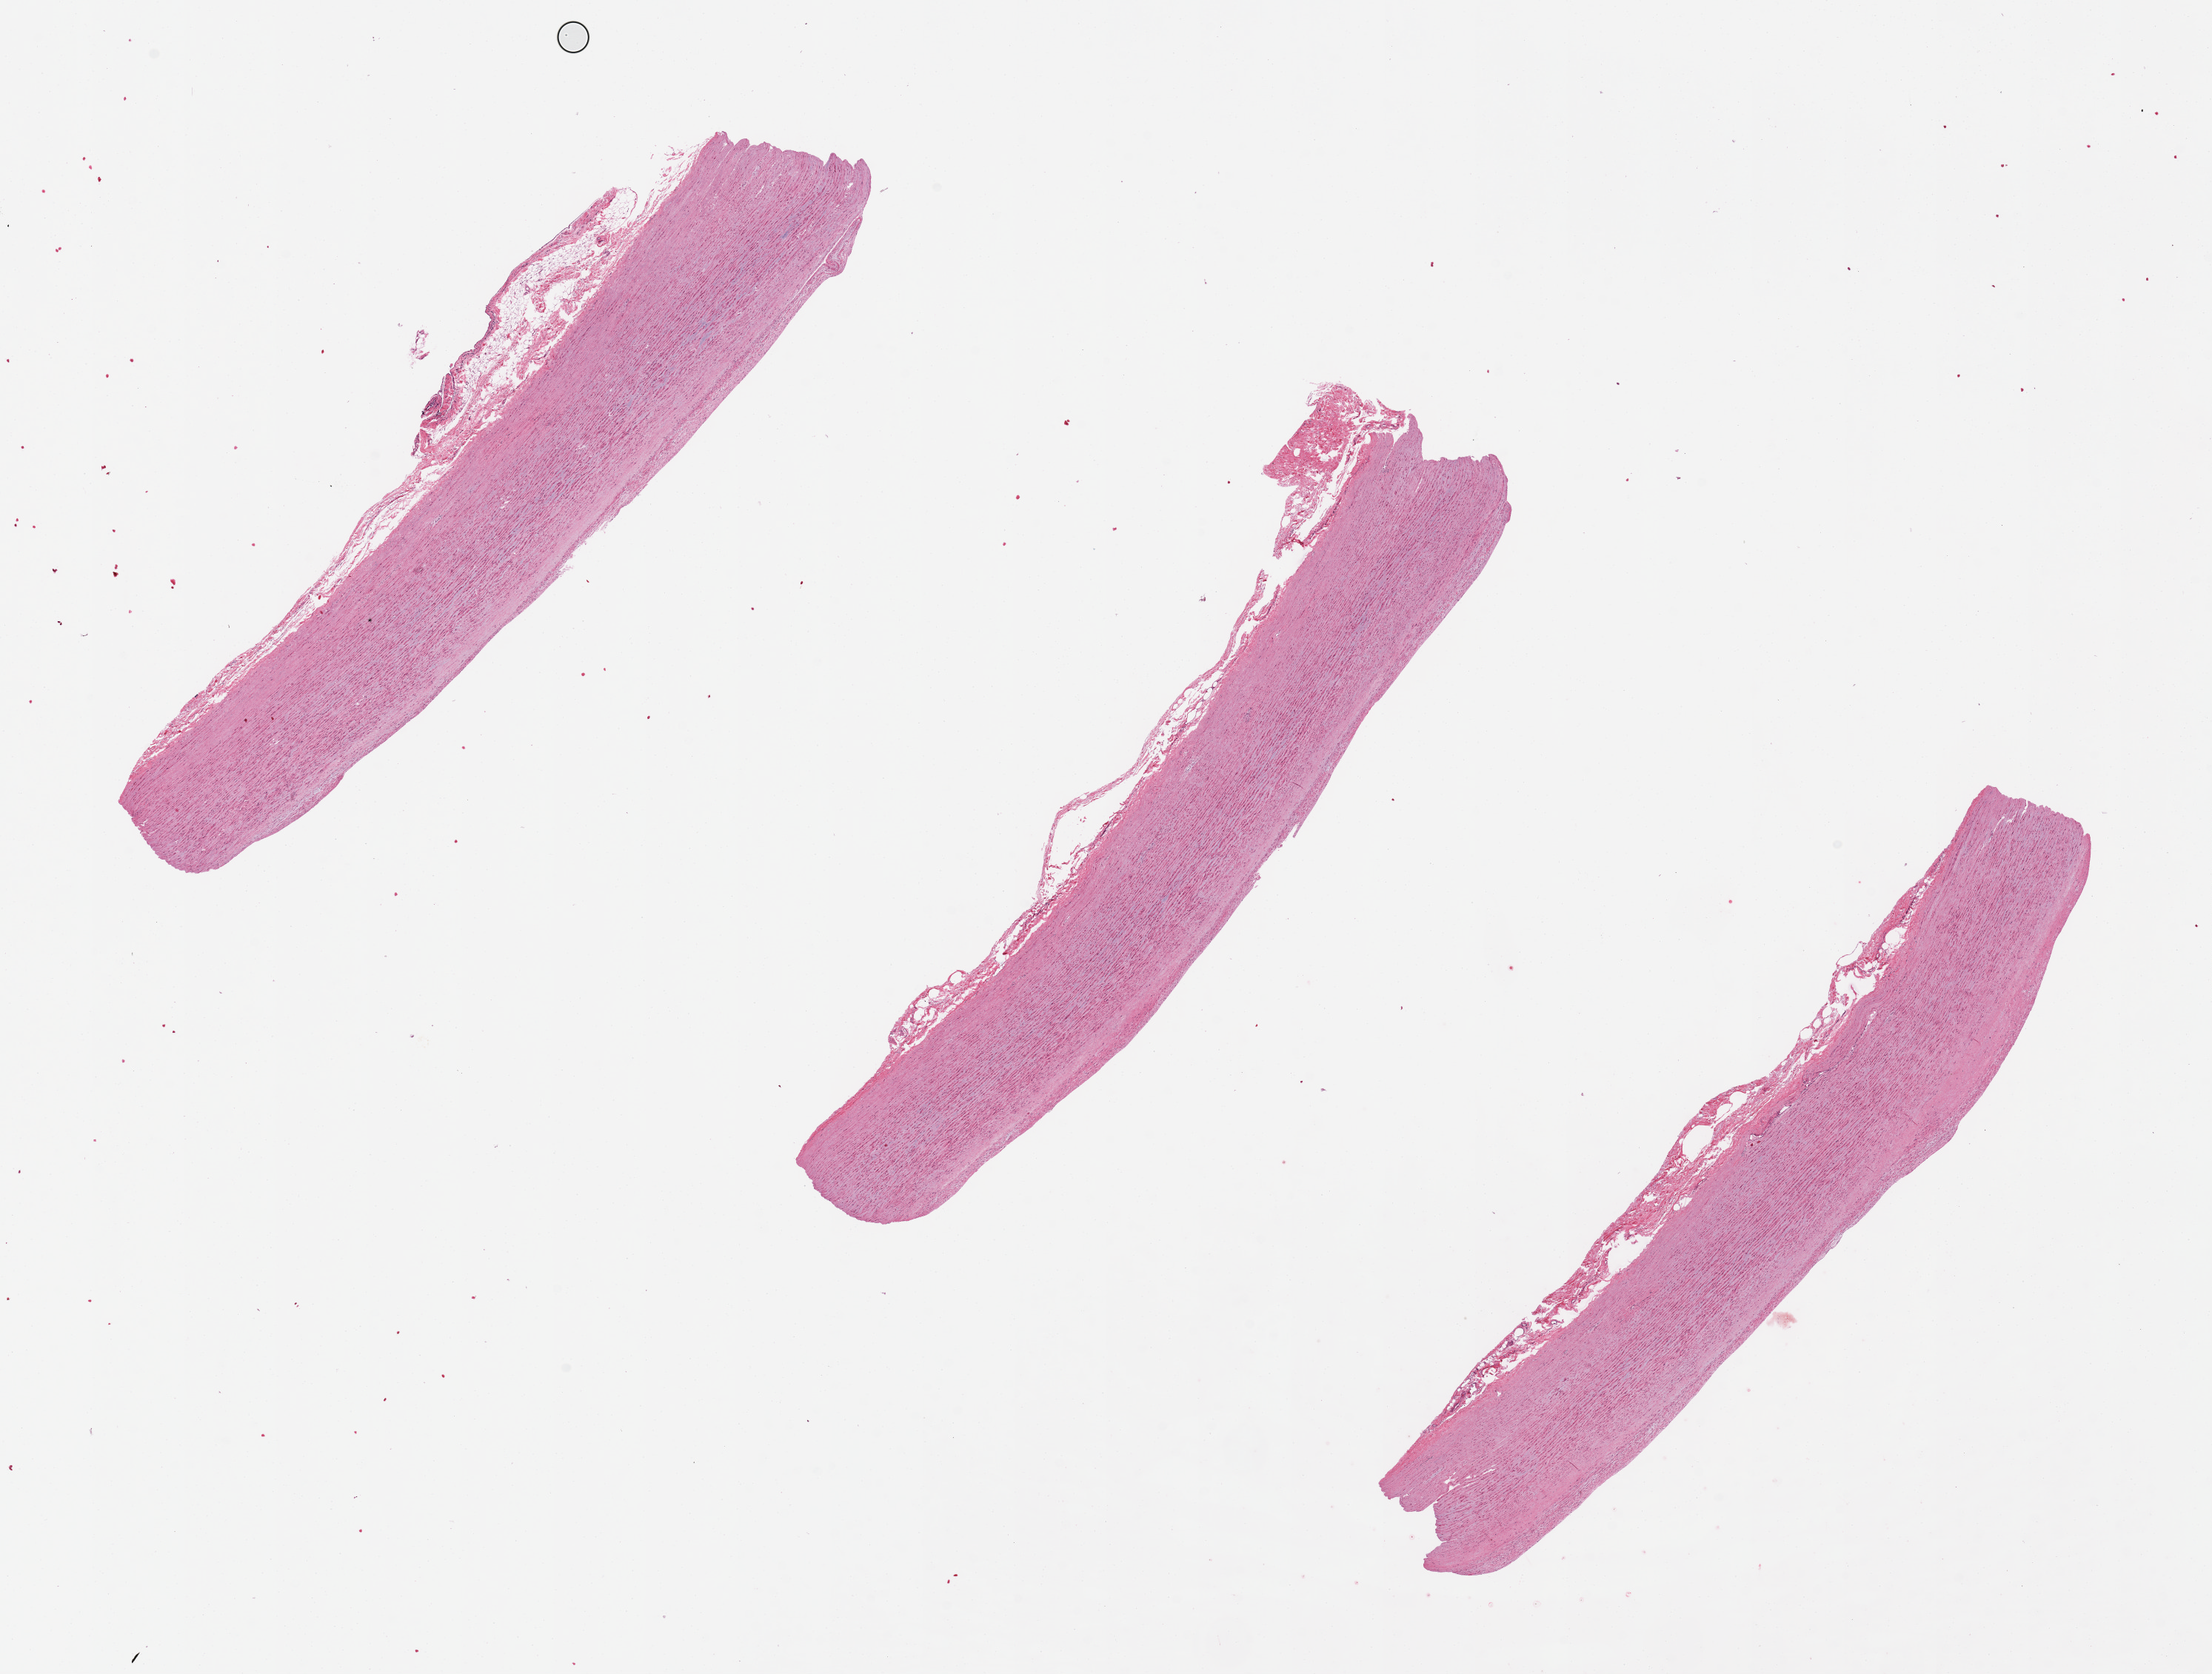
Whole-slide image, haematoxylin and eosin stain — low-resolution overview of the scanned area, about 23.6 x 17.9 mm (slide scanned at 20x). PAXgene-fixed, paraffin-embedded tissue. Section of aorta (target tissue). Donor tissue sample. Donor: male.
- pathologist's review note for this sample: Thickness averages 1.8mm. Endothelium largely sloughed